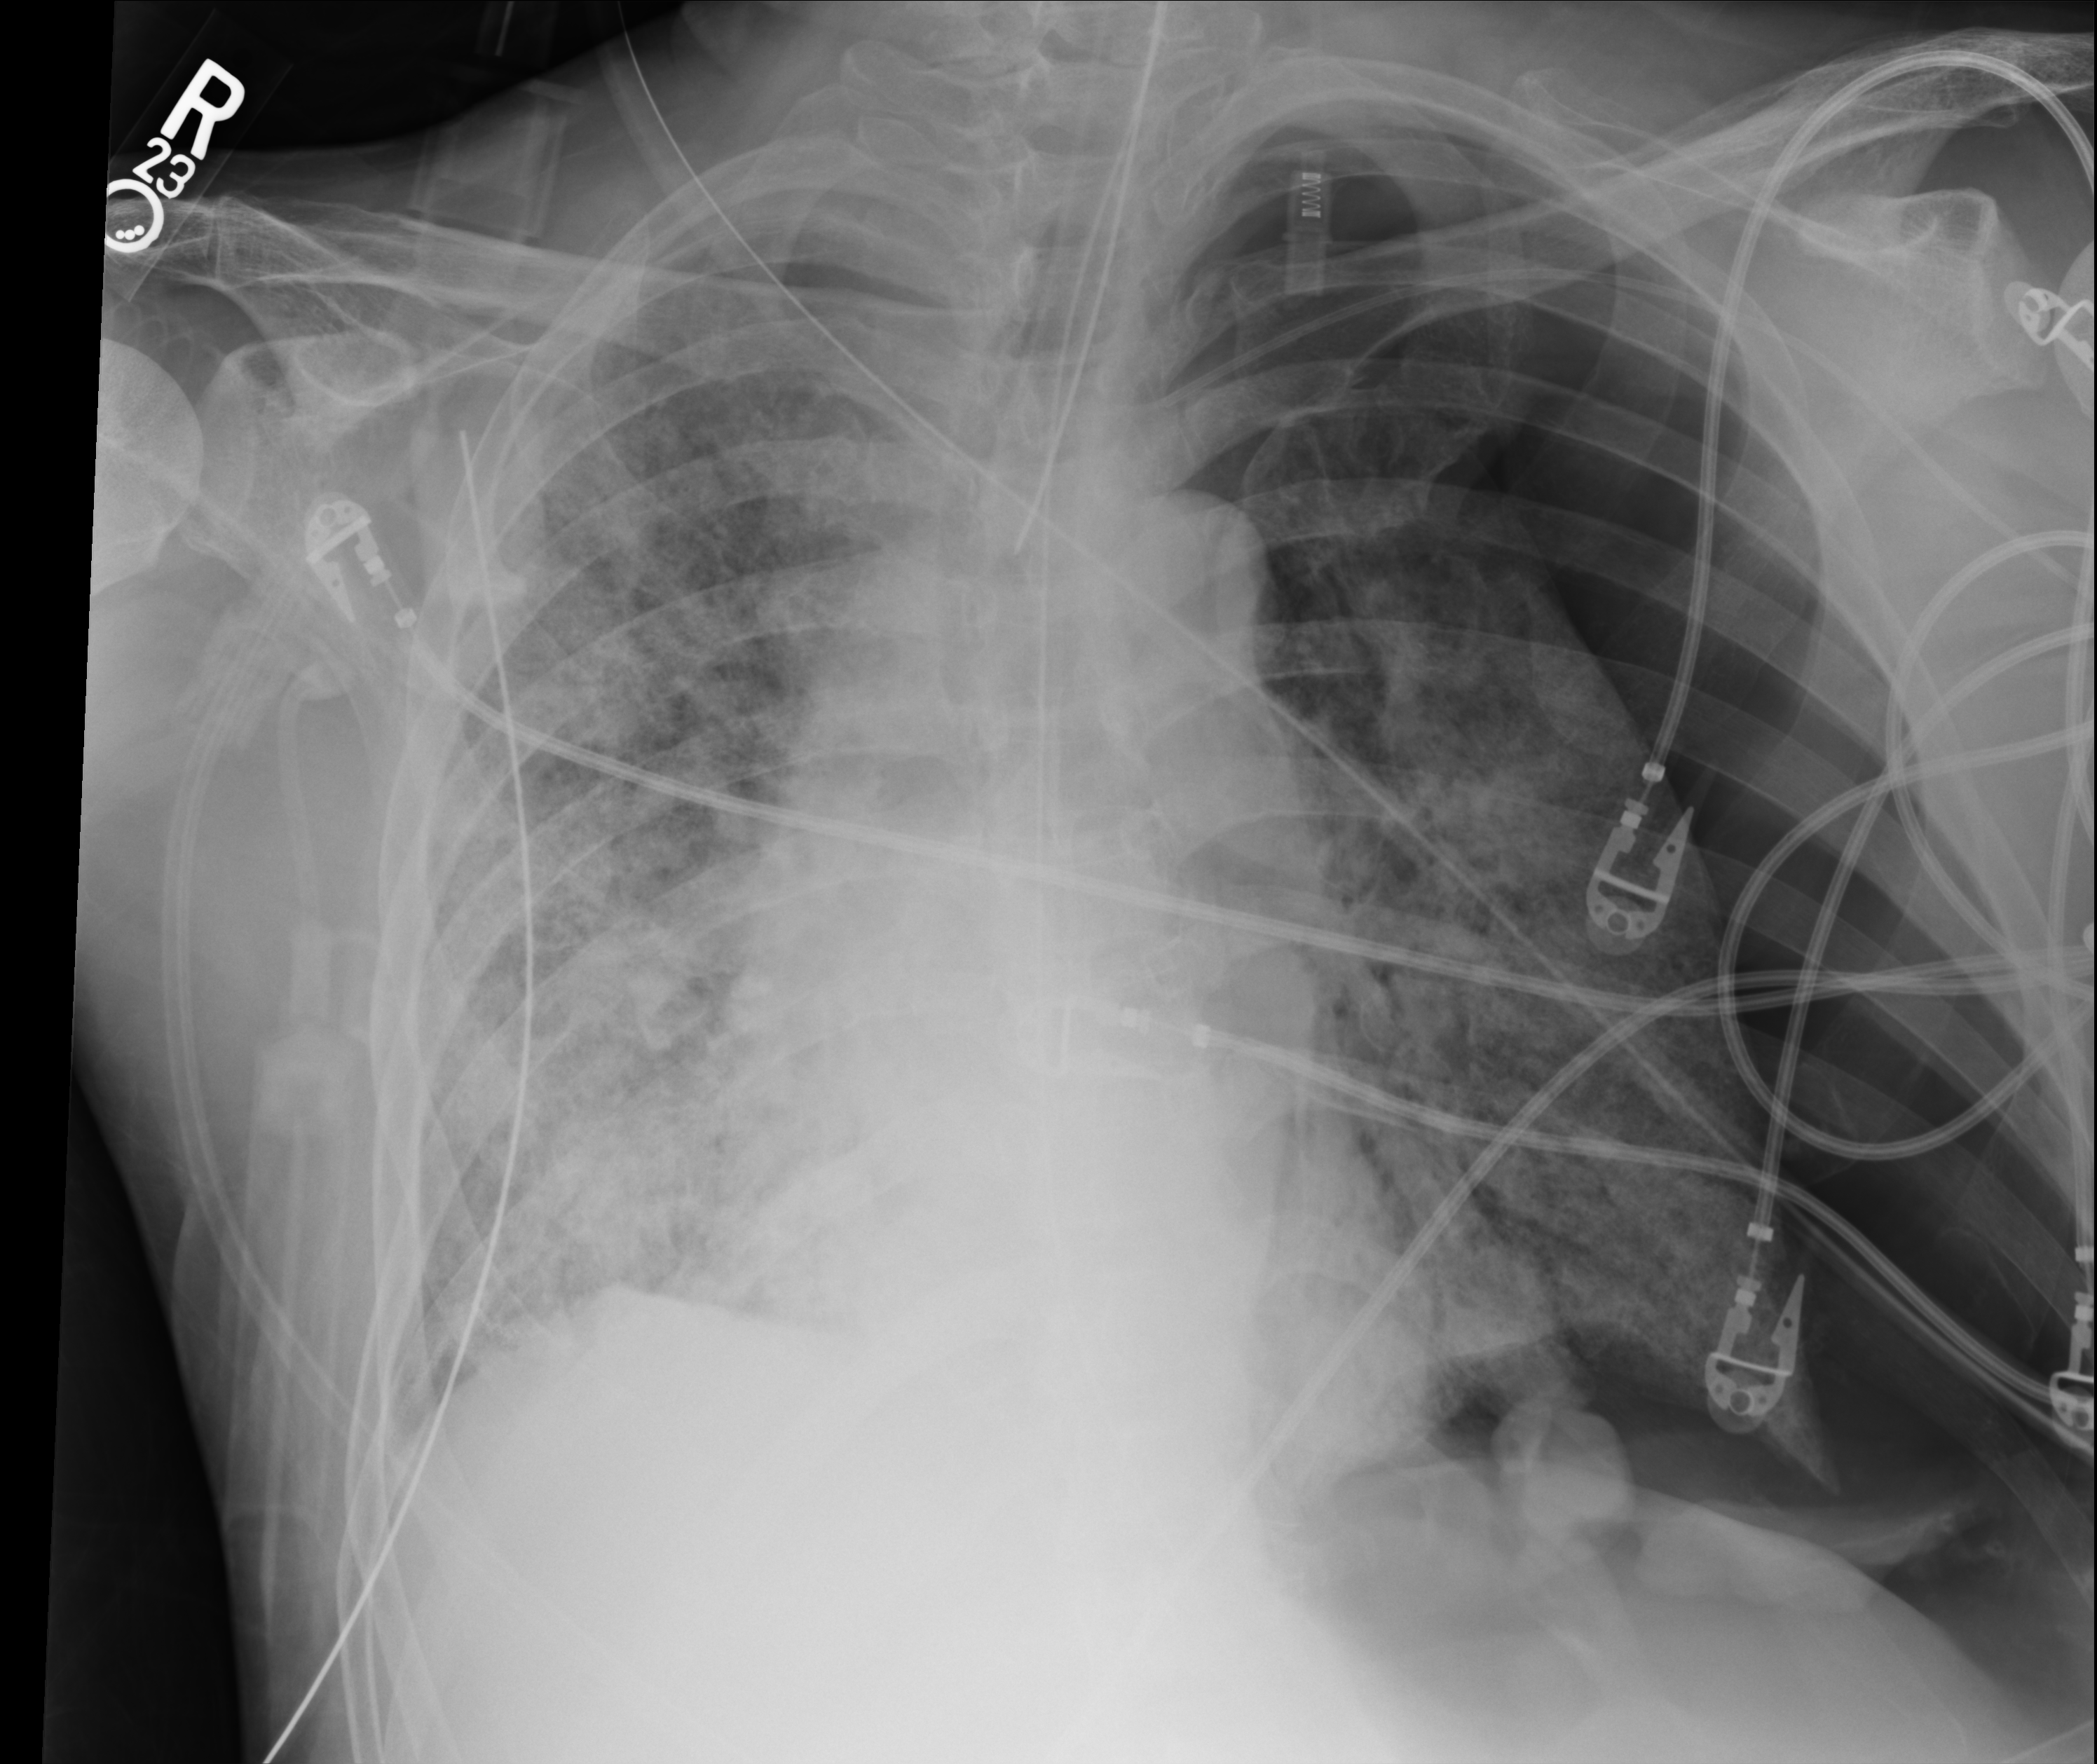
Chest X-ray (portable); anteroposterior (AP) projection. Male patient hospitalised with COVID-19, age 60–74 years.
Hospital-stay facts (about this admission, not read from this image; timing relative to this image not recorded): mechanically ventilated during this hospital stay: yes.